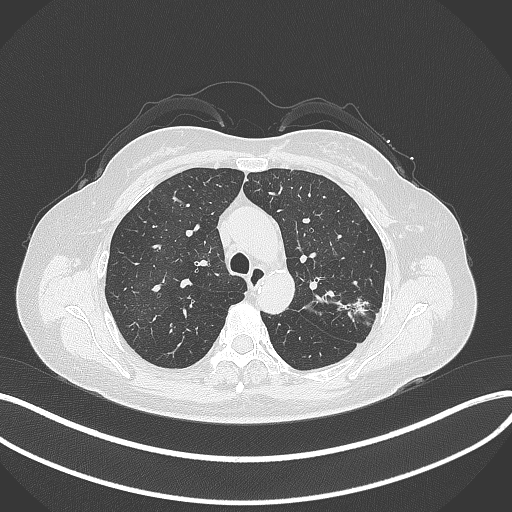
Chest CT, one axial slice. Position 234 of 319 along the scan axis. Lung window (W 1500 / L -600 HU). 1 mm slice thickness. 512 × 512 image matrix. Female patient, age 60 years. Case-level facts recorded for this patient, not image findings: clinical TNM (as recorded): T1c N0 M0.
Annotated regions visible in this slice (rectangle marked by the reading radiologist):
- lung tumour (recorded histology: adenocarcinoma): bounding box [x1, y1, x2, y2] px = [343, 293, 370, 328]